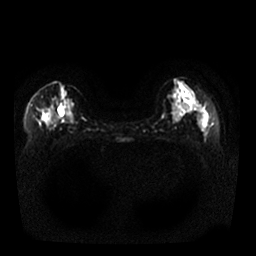
Breast MRI, one axial slice; position 11 of 25 along the scan axis; diffusion-weighted series; image 2 of 4 stored at this slice position (different b-values; order by instance number); 1.5 T; 4 mm slice thickness; 256 × 256 image matrix, field of view 340 × 340 mm. Female patient.
Annotated regions visible in this slice (expert manual segmentation):
- tumour on diffusion-weighted imaging: box from (x=43, y=115) to (x=52, y=126) px